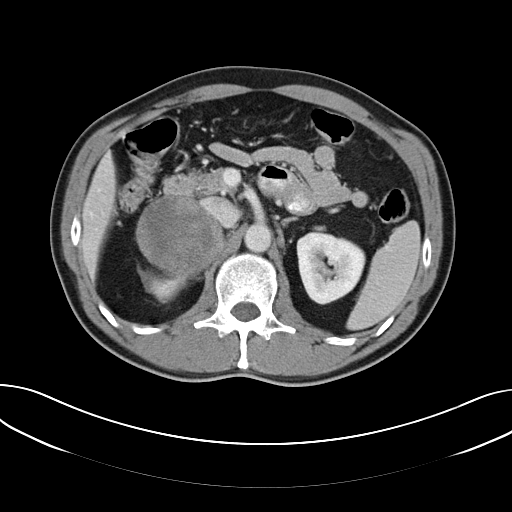
Contrast-enhanced abdominal CT, one axial slice. Position 32 of 61 along the scan axis. Reconstruction kernel B40f. 120 kVp. Intravenous contrast given. Soft-tissue window (W 400 / L 40 HU). 5 mm slice thickness. 512 × 512 image matrix, field of view 372 × 372 mm. Patient: male, 57 years. From the clinical record (not read from this slice): diagnosis: adrenocortical carcinoma; tumour side: right adrenal.
Outlined on this slice (semi-automatic segmentation, software-assisted and operator-edited):
- mass: bounding box <137,198,220,277> (left, top, right, bottom; pixels)